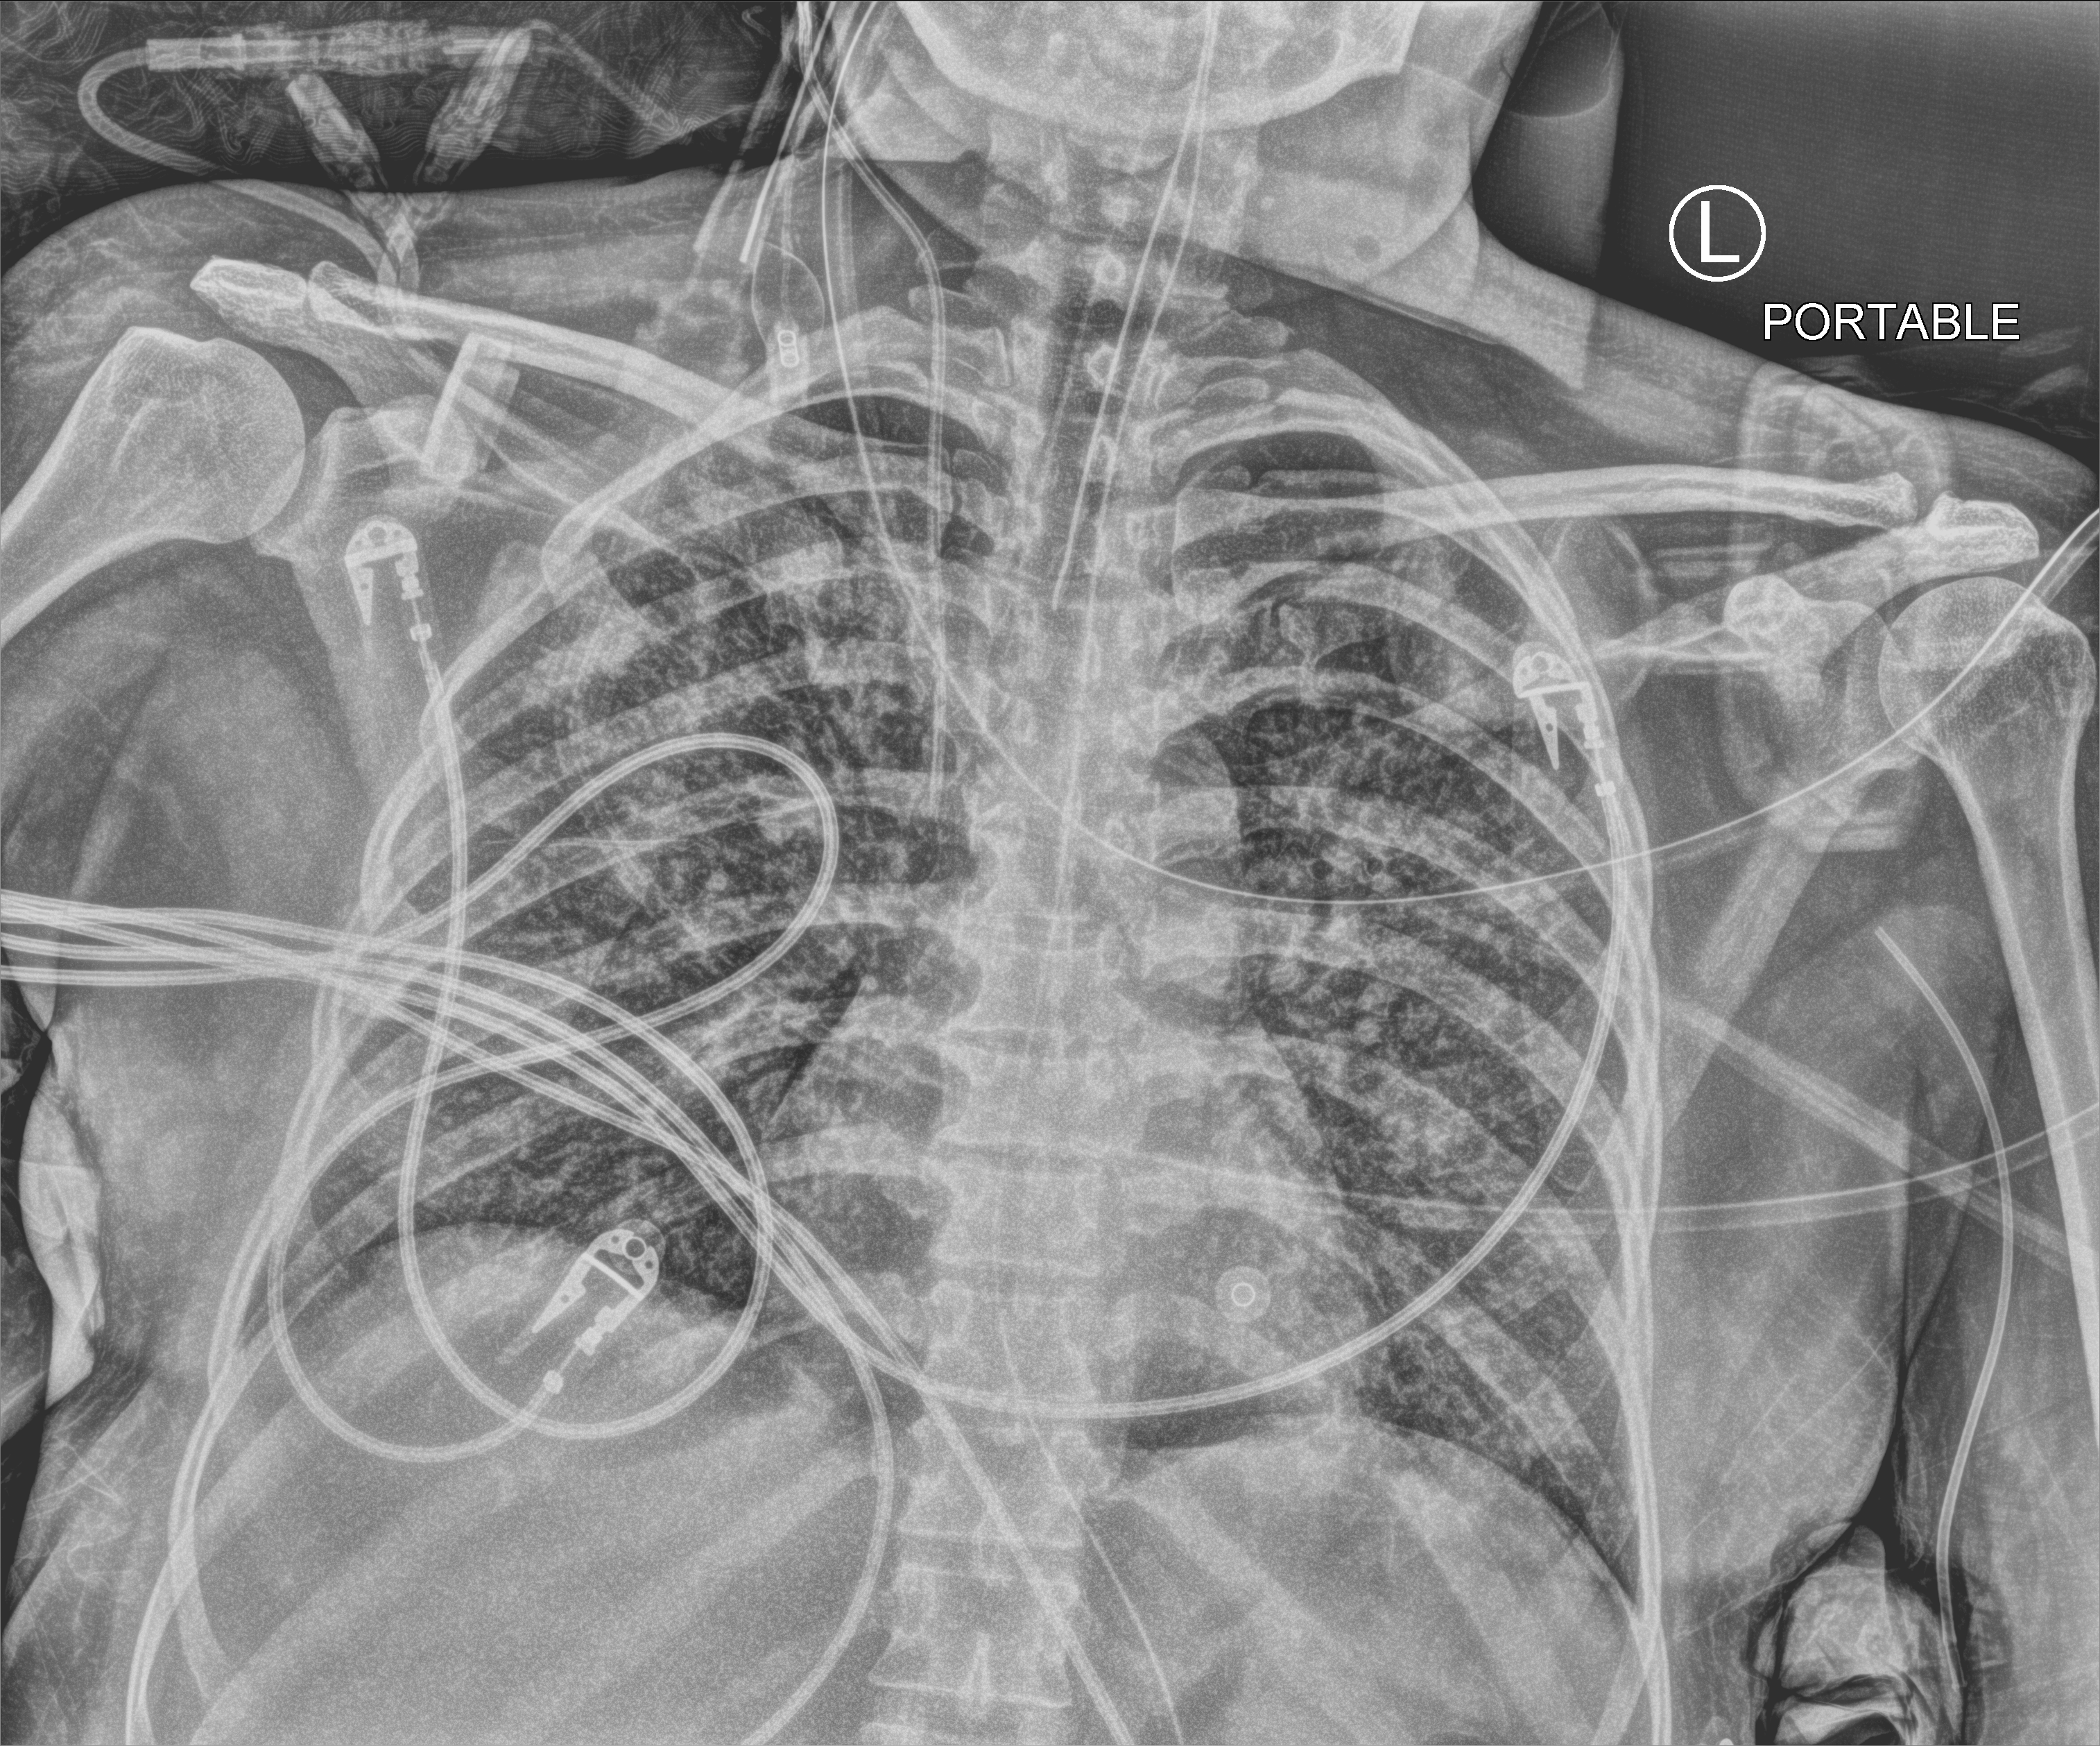
Portable chest radiograph, anteroposterior (AP) projection. Patient hospitalised with COVID-19; female, aged 18–59 years.
From the hospital-stay record, not from the radiograph (when in the stay this image was taken is not recorded): hypertension (admission record): no; other chronic lung disease (admission record): no; mechanically ventilated during this hospital stay: yes.